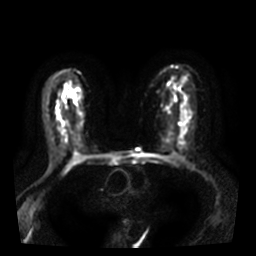
Breast MRI, one axial slice. Position 21 of 38 along the scan axis. Diffusion-weighted series; image 2 of 4 stored at this slice position (different b-values; order by instance number). 3 T. 5 mm slice thickness. 256 × 256 image matrix. Female patient.
Annotated regions visible in this slice (outlined manually by an expert reader):
- tumour on diffusion-weighted imaging: bounding box <72,94,76,102> (left, top, right, bottom; pixels)